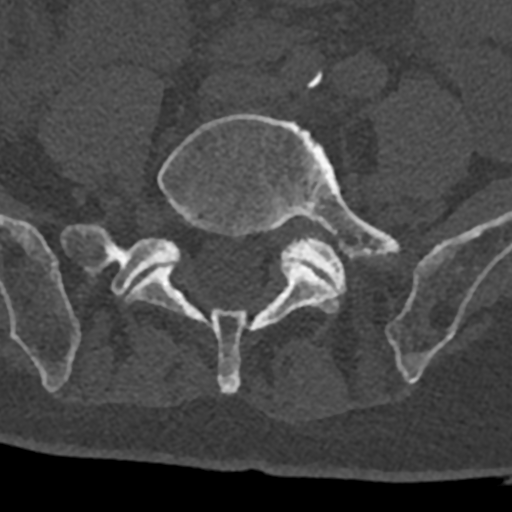
CT including the spine, one axial slice; slice 190 of 797 in the series (ordered by position); reconstruction kernel Br40s/3; bone window (W 1800 / L 400 HU); 0.5 mm slice thickness; 512 × 512 image matrix, field of view 160 × 160 mm. Male patient, age 74 years. Case-level facts recorded for this patient, not image findings: primary cancer: renal; vertebrae with lytic lesions (as recorded): T10, L1, L2, L3, L4, L5.
Outlined on this slice (semi-automatically segmented with operator editing):
- L5 vertebra: box from (x=127, y=113) to (x=401, y=394) px